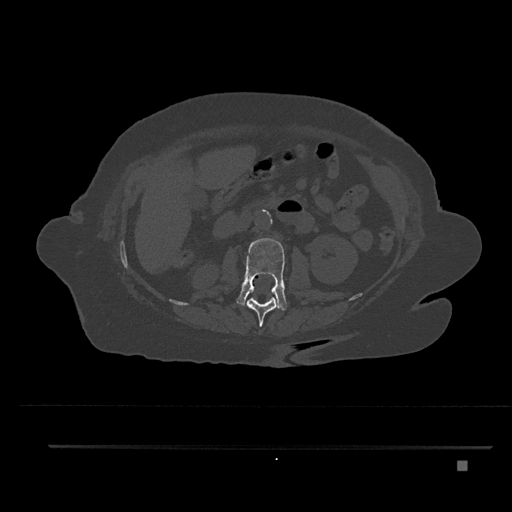
CT including the spine, one axial slice. Position 192 of 797 along the scan axis. Reconstruction kernel Br40s/3. 120 kVp. Bone window (W 1800 / L 400 HU). 0.5 mm slice thickness. 512 × 512 image matrix. Female patient, age 76 years. Case-level facts recorded for this patient, not image findings: primary cancer: lung; vertebrae with lytic lesions (as recorded): T11, L3.
Structures marked on this image (semi-automatic segmentation, software-assisted and operator-edited):
- L1 vertebra: bounding box [x1, y1, x2, y2] px = [247, 297, 279, 327]
- L2 vertebra: [237, 237, 287, 311]